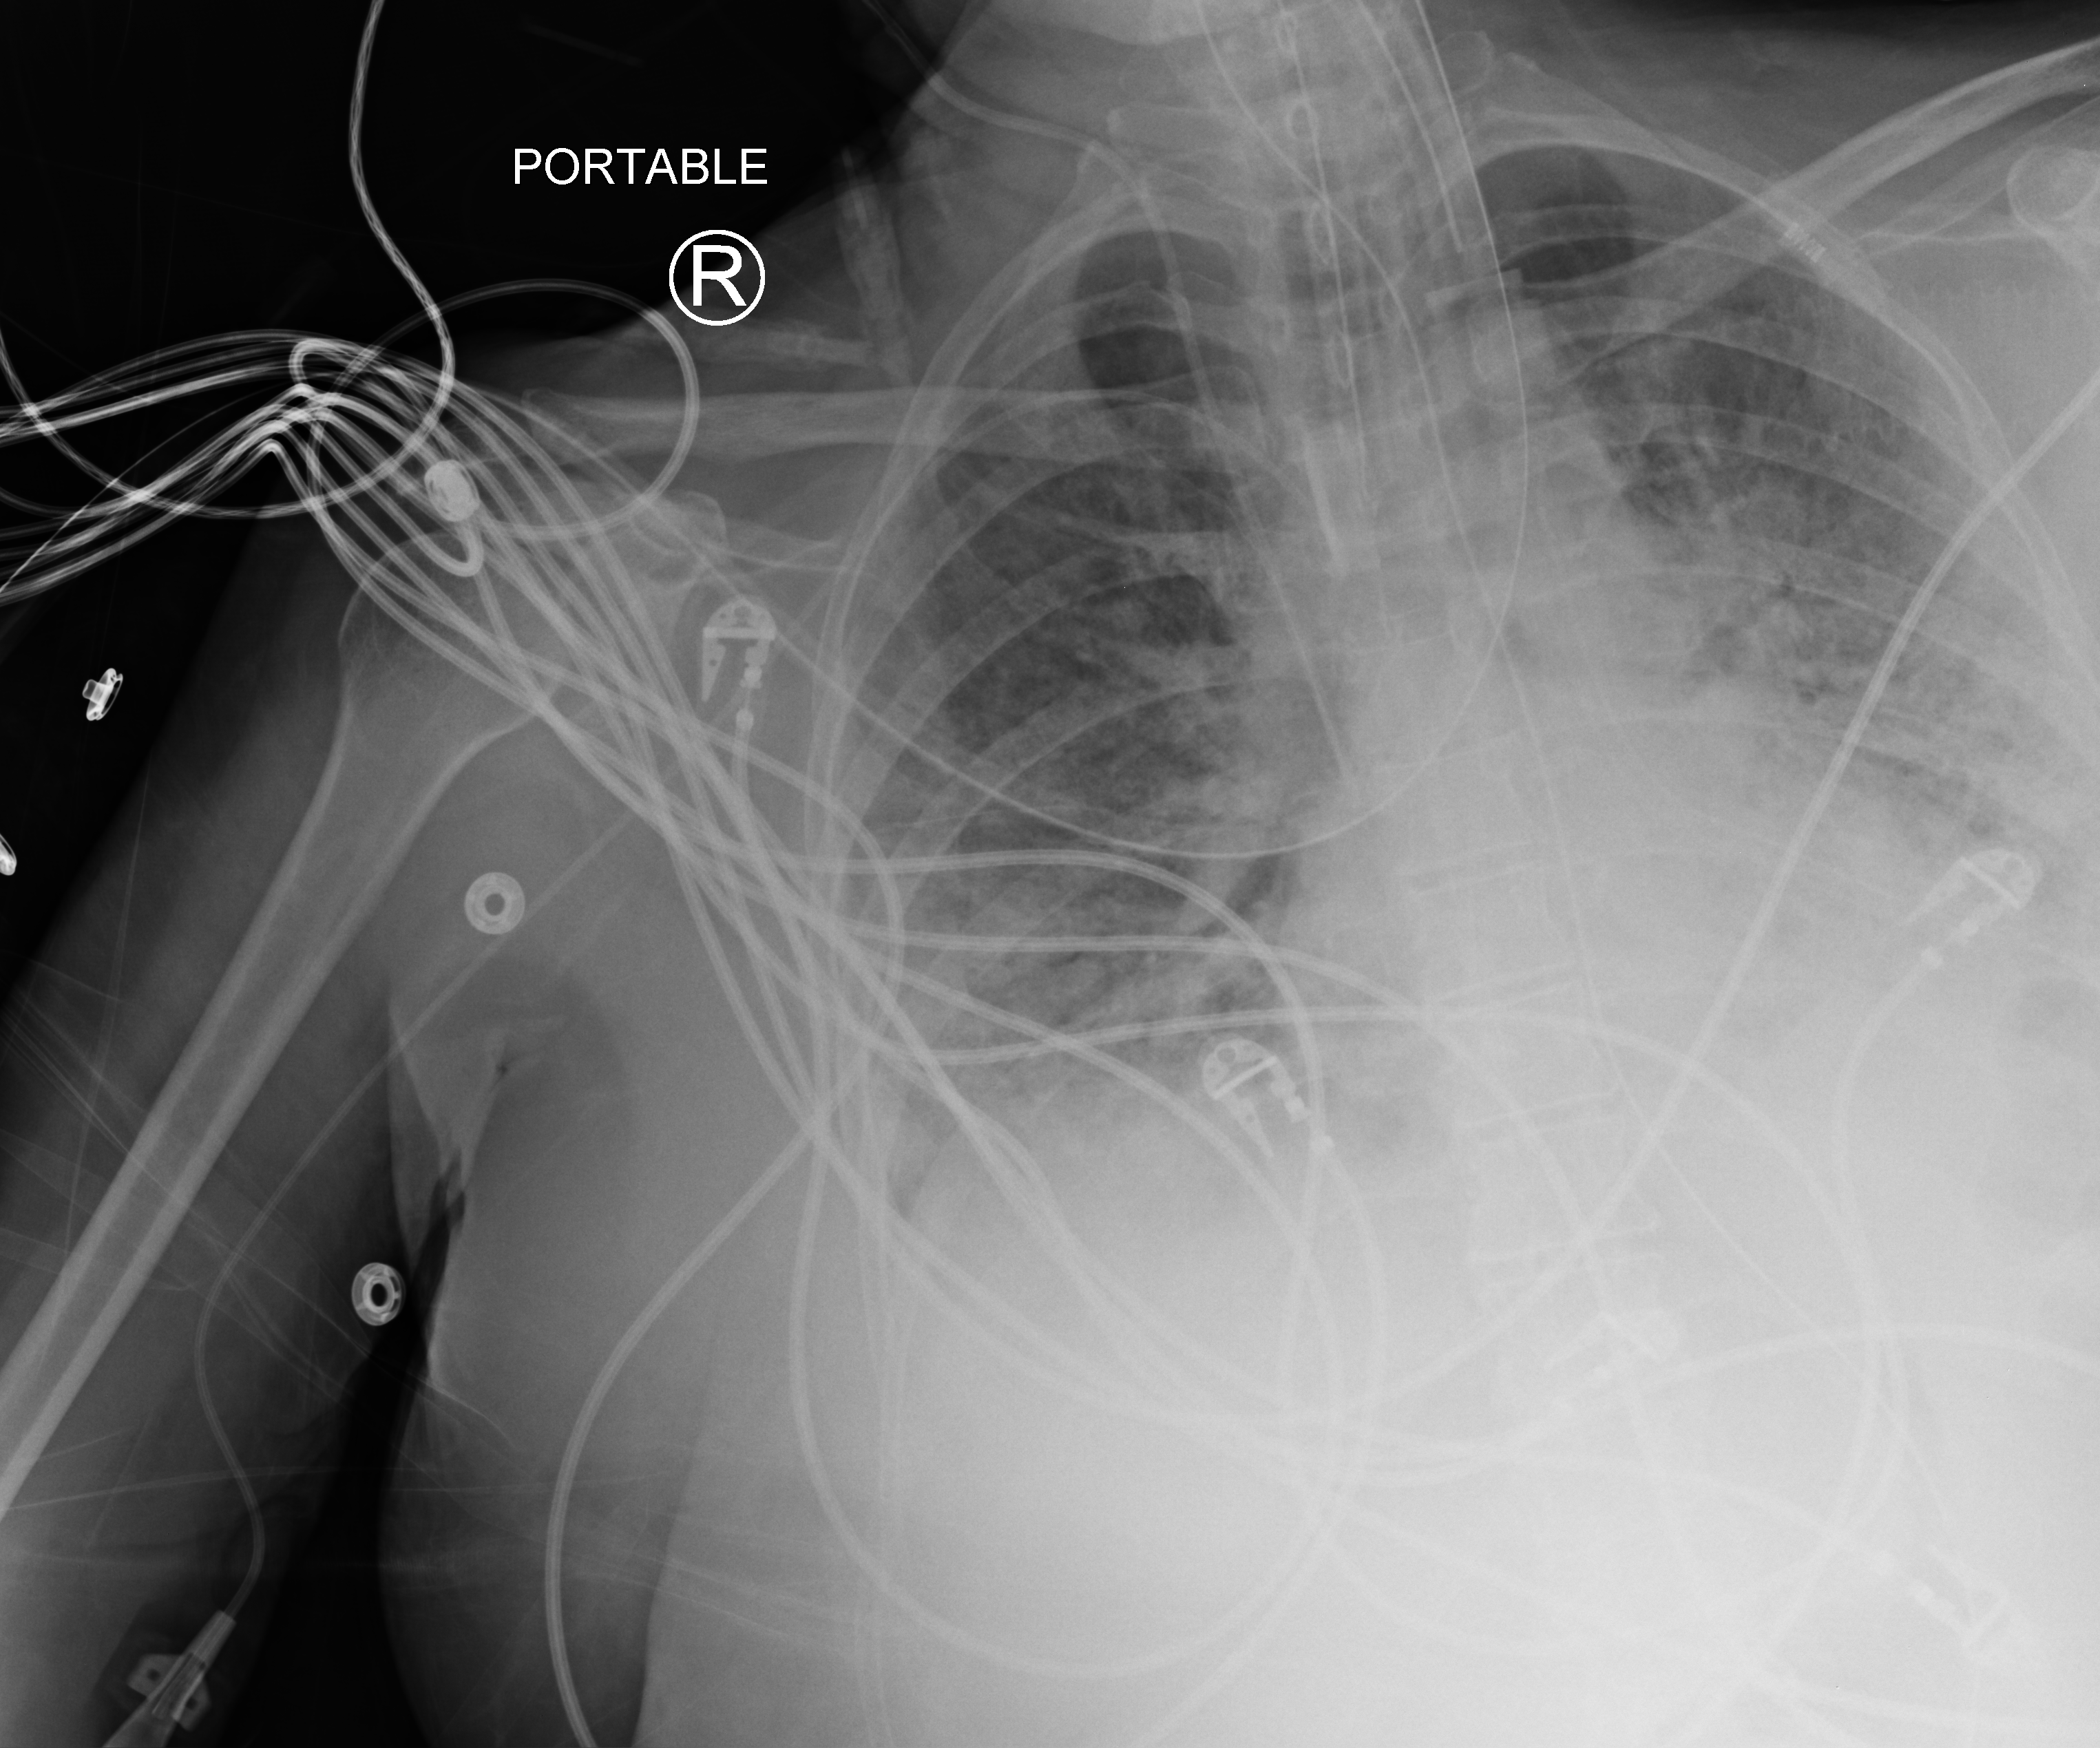
Bedside chest radiograph (computed radiography); anteroposterior (AP) projection. Patient hospitalised with COVID-19; female, aged 60–74 years.
Hospital-stay facts (about this admission, not read from this image; timing relative to this image not recorded): mechanically ventilated during this hospital stay: yes.